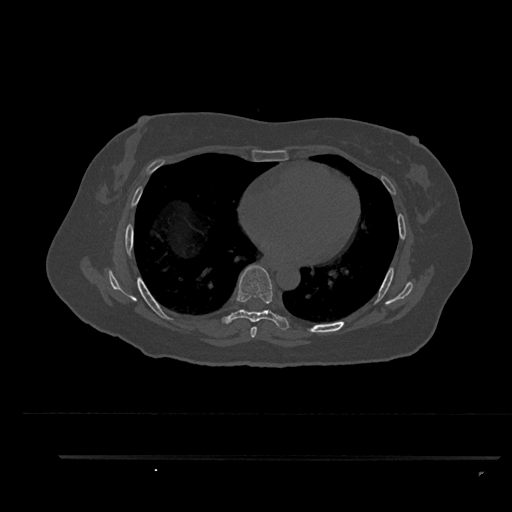
CT including the spine, one axial slice; slice 511 of 797 in the series (ordered by position); bone window (W 1800 / L 400 HU); 0.5 mm slice thickness; 512 × 512 image matrix, field of view 408 × 408 mm. Female patient, age 44 years. From the clinical record (not read from this slice): primary cancer: renal.
Structures marked on this image (semi-automatic segmentation, software-assisted and operator-edited):
- T6 vertebra: bounding box [x1, y1, x2, y2] px = [250, 326, 257, 338]
- T7 vertebra: [222, 265, 289, 330]